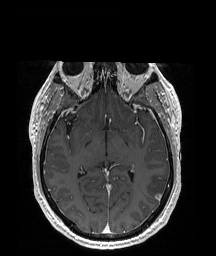
Brain MRI from a brain-tumour surgery series, one axial slice. Slice 108 of 192 in the series (ordered by position). T1-weighted post-contrast. 216 × 256 image matrix. From the clinical record (not read from this slice): histopathology: Glioblastoma; WHO grade: 4; IDH mutation: no; tumour location: Left Temporal Parietal.
Structures marked on this image (outlined manually by an expert reader):
- tumour: bounding box [x1, y1, x2, y2] px = [146, 174, 166, 199]